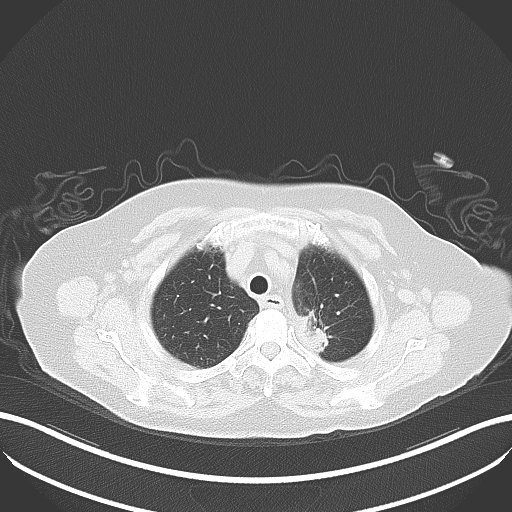
Chest CT, one axial slice; reconstruction kernel B80f; lung window (W 1500 / L -600 HU); 5 mm slice thickness; 512 × 512 image matrix, field of view 400 × 400 mm. Female patient, age 81 years. From the clinical record (not read from this slice): clinical TNM (as recorded): T2a N0 M0.
Outlined on this slice (bounding box drawn by a radiologist):
- lung tumour (recorded histology: adenocarcinoma): box from (x=294, y=306) to (x=334, y=364) px